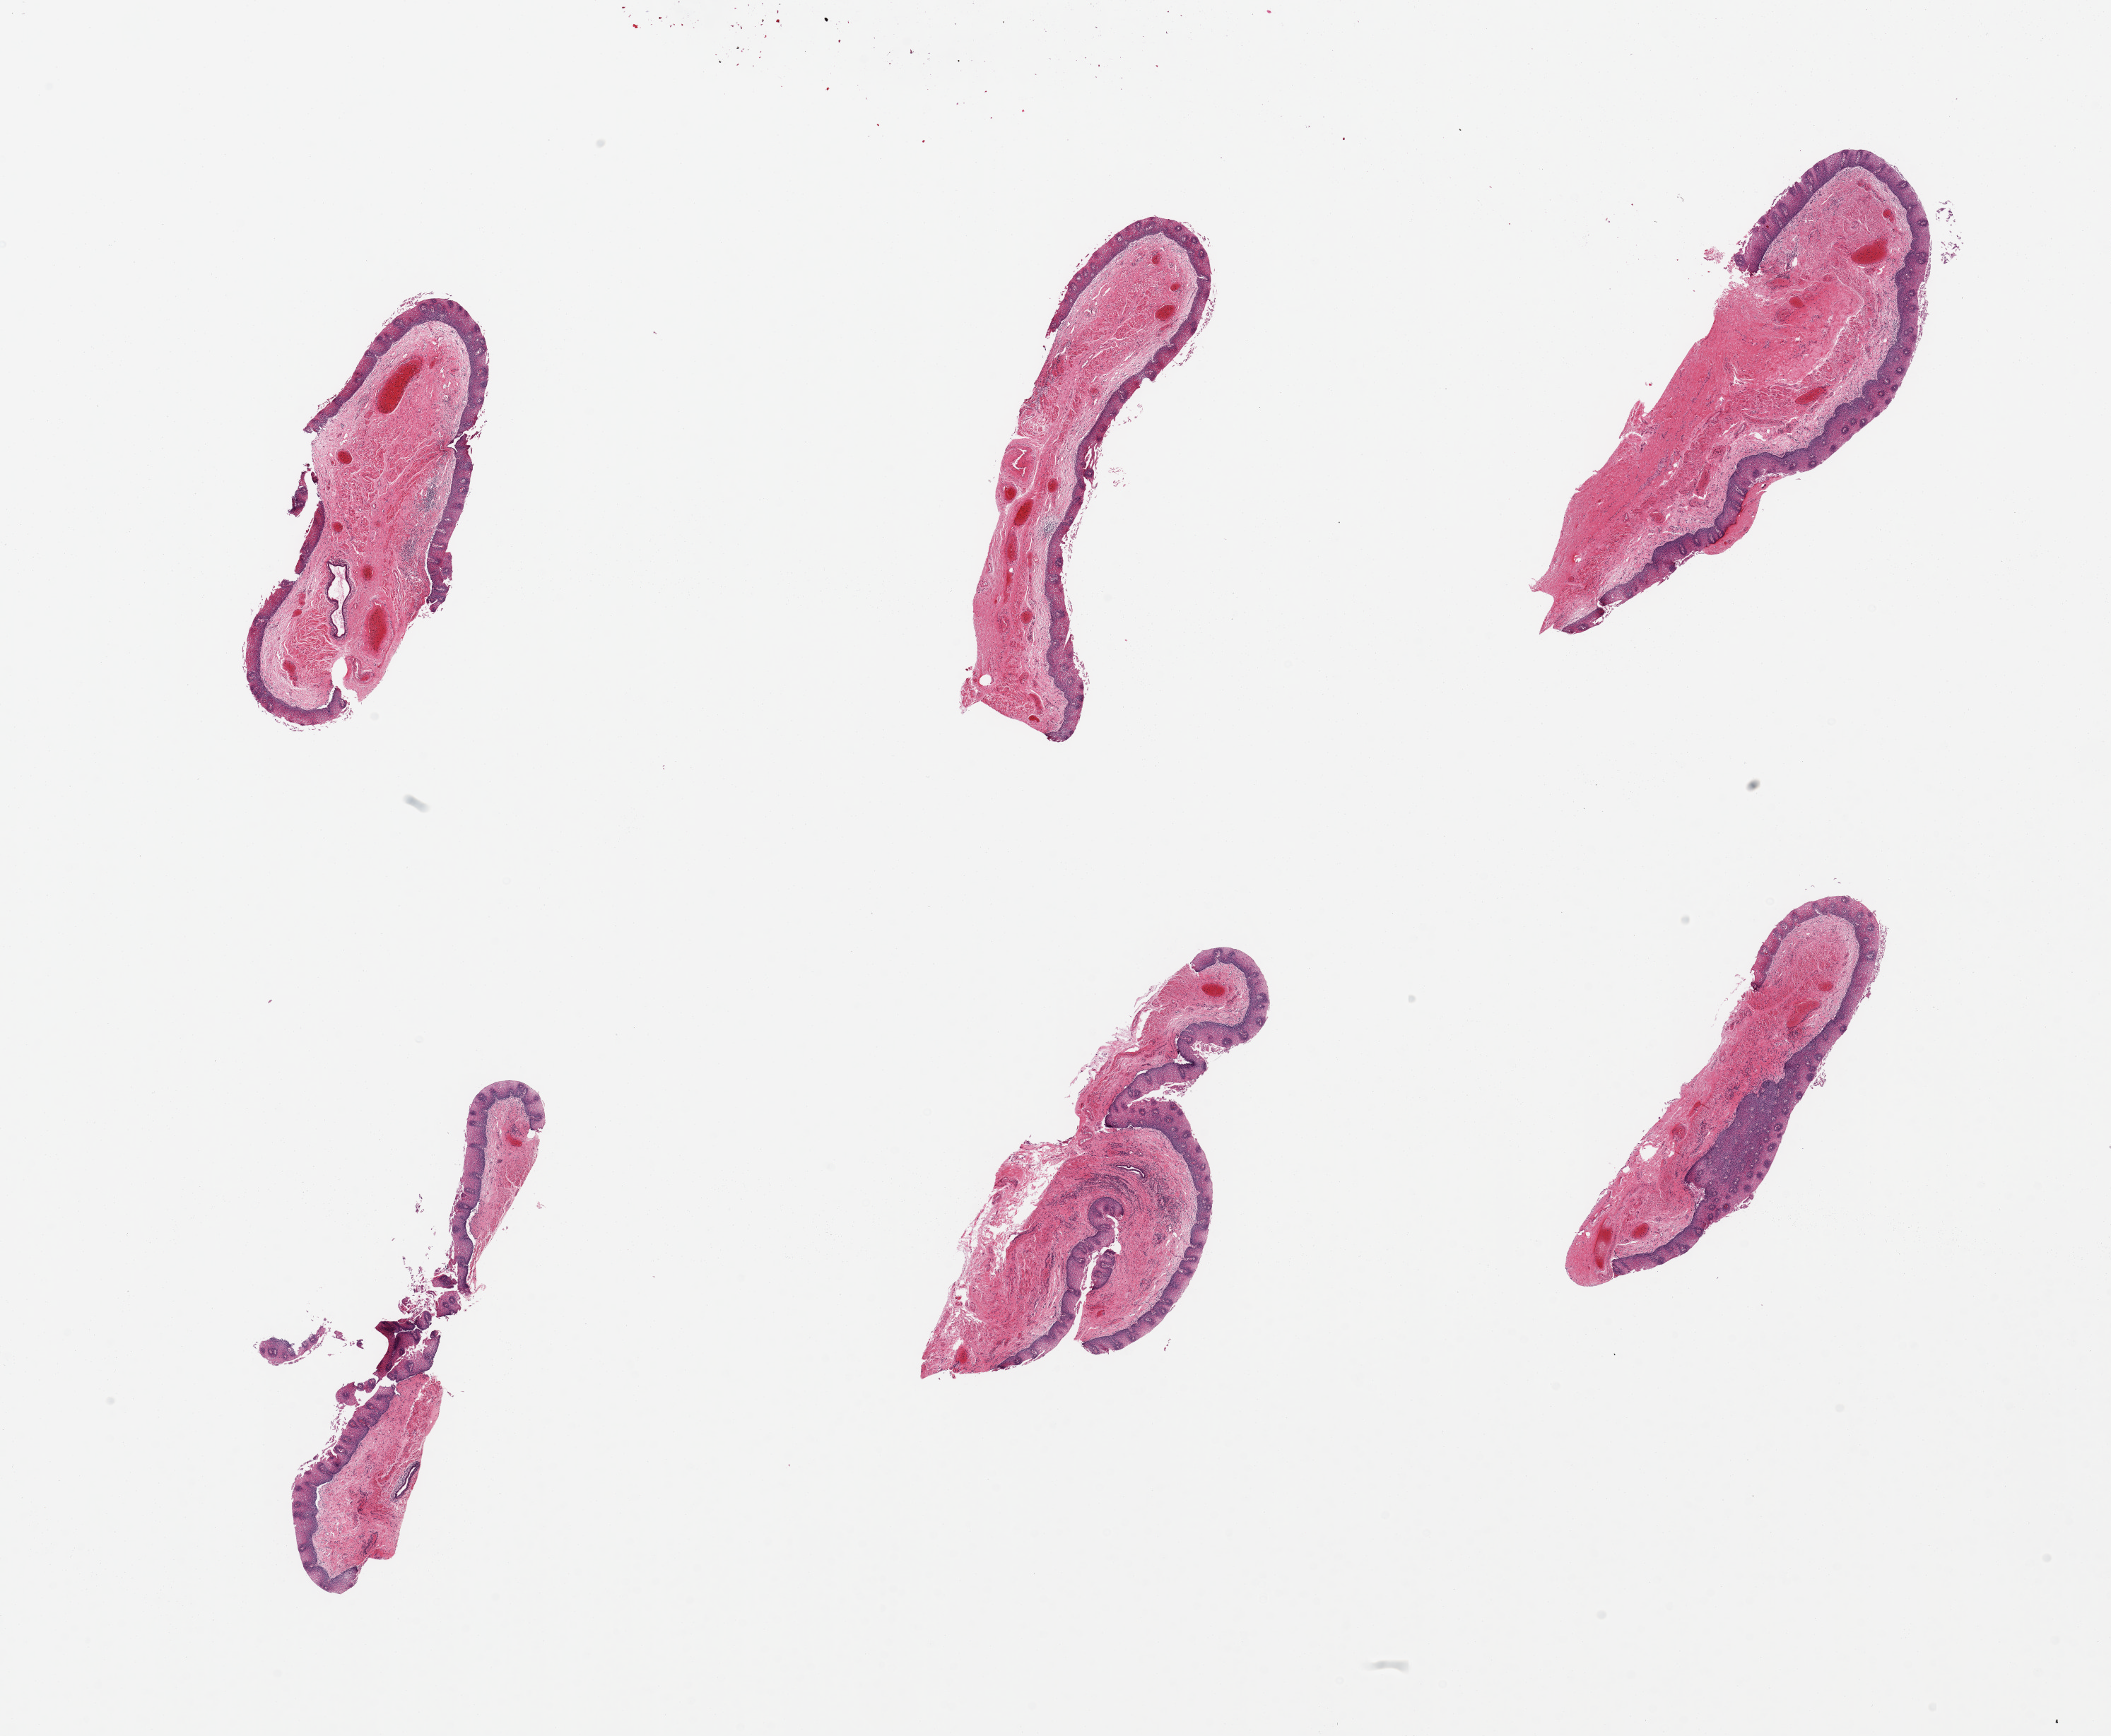
Whole-slide image, haematoxylin and eosin stain, a low-resolution overview of the entire scanned area, about 23.6 x 19.4 mm; PAXgene-fixed, paraffin-embedded tissue; target tissue: esophageal mucous membrane; donor tissue sample. Female donor.
- review note (as recorded): 6 pieces, squamous mucosa up to ~0.35mm, ~15% of thickness